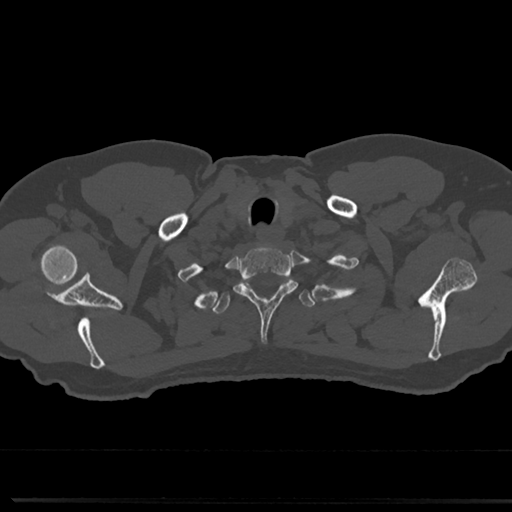
CT including the spine, one axial slice. Reconstruction kernel Br40s/3. 120 kVp. Bone window (W 1800 / L 400 HU). 0.5 mm slice thickness. 512 × 512 image matrix, field of view 355 × 355 mm. Male patient, age 61 years. Case-level facts recorded for this patient, not image findings: primary cancer: prostate.
Annotated regions visible in this slice (semi-automatically segmented with operator editing):
- T1 vertebra: bounding box <234,247,297,319> (left, top, right, bottom; pixels)
- T2 vertebra: <212,277,315,316>